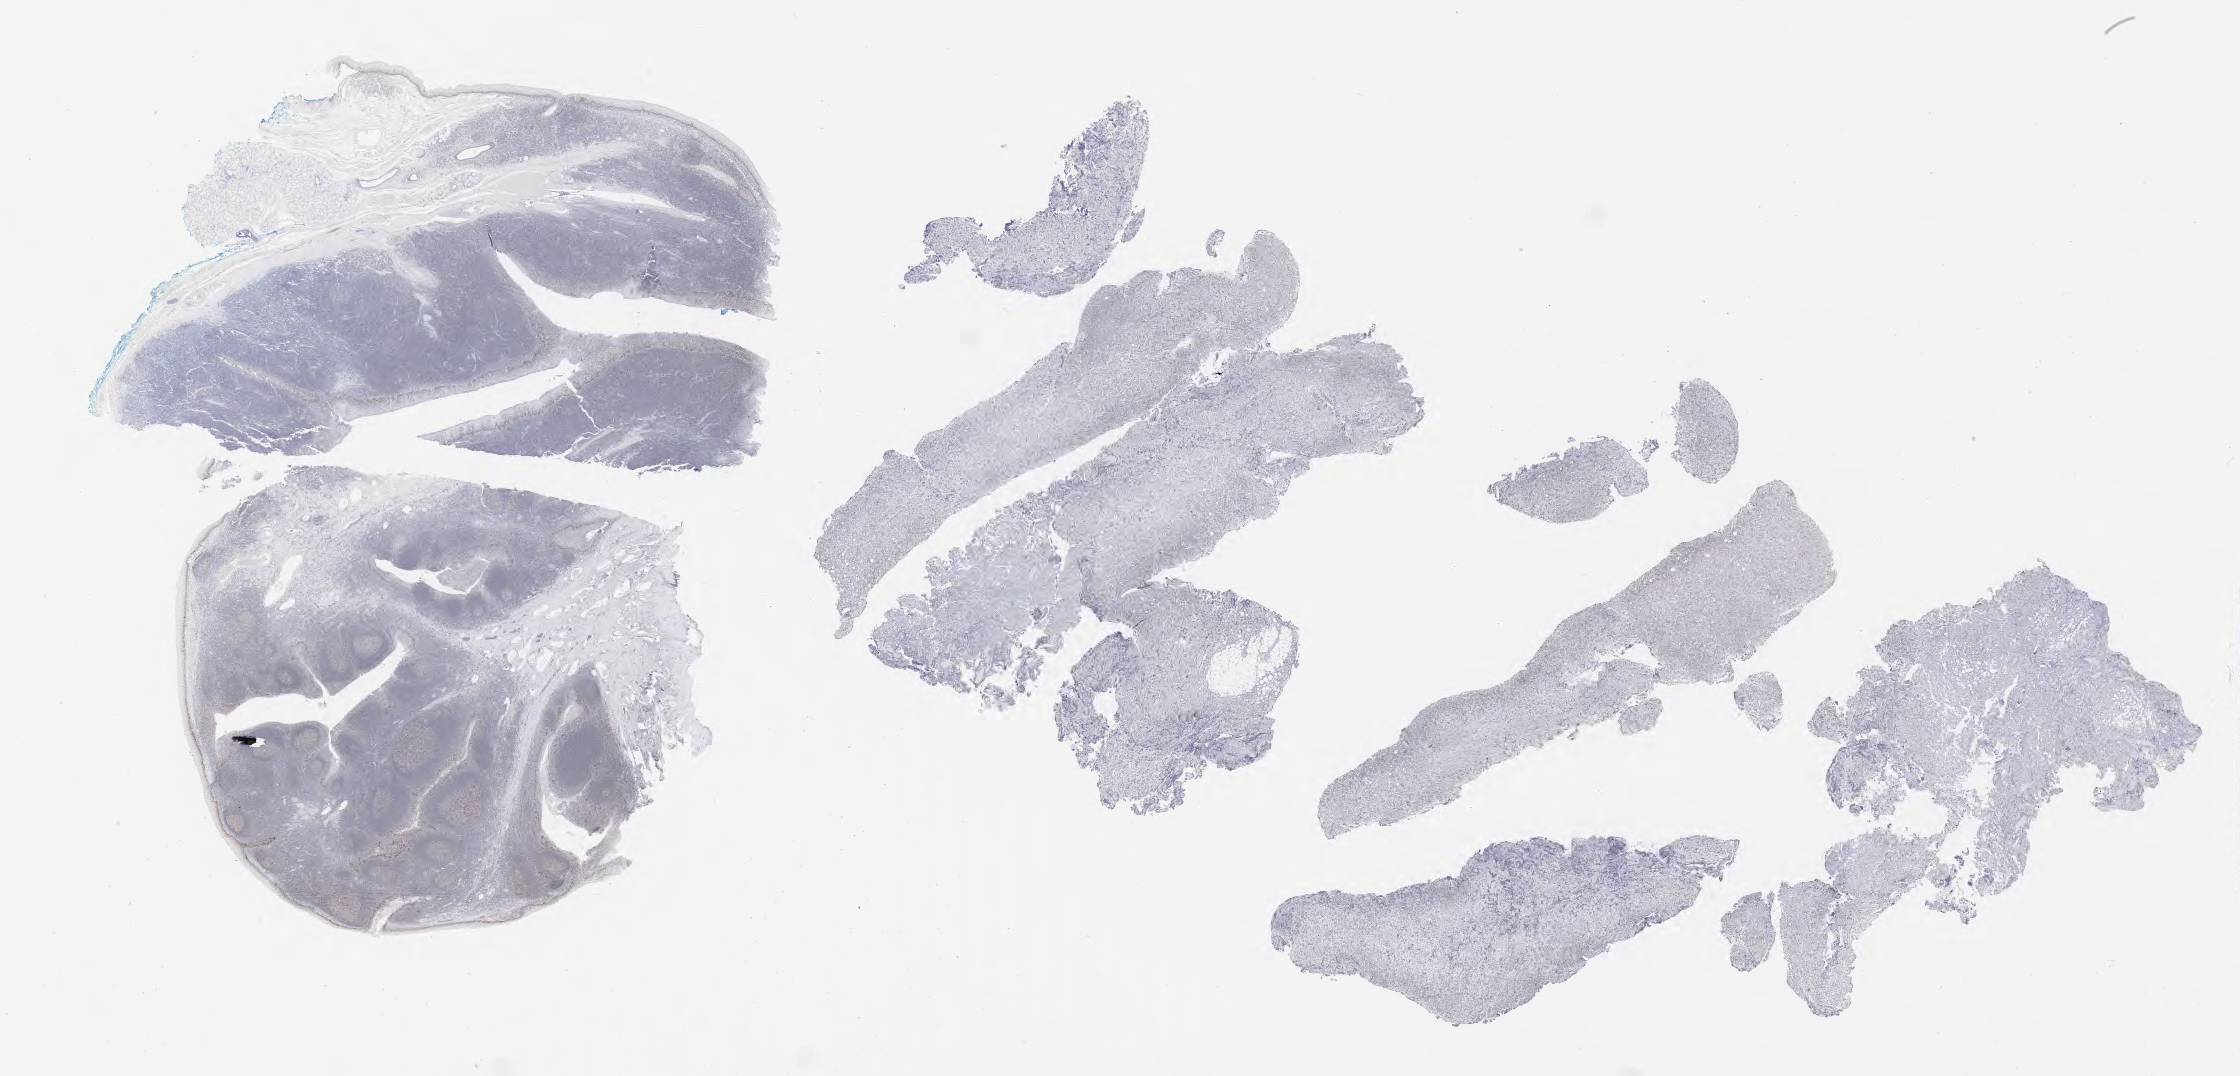
IHC for p53, whole-slide image, whole scanned area (about 36.2 x 17.4 mm) shown as a low-resolution overview; specimen: tumor tissue. Patient: male, 45 years old.
* histologic diagnosis: Diffuse large B-cell lymphoma, NOS